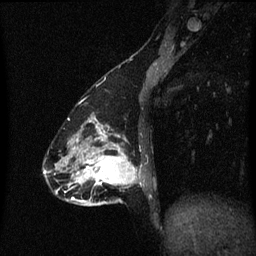
Breast MRI (dynamic contrast-enhanced), one sagittal slice; position 19 of 60 along the scan axis; dynamic contrast-enhanced series, image 2 of 3 at this slice position (ordered by acquisition); 1.5 T; TE 4.2 ms, TR 8.4 ms; 256 × 256 image matrix, field of view 200 × 200 mm. Patient: female, 47 years.
Structures marked on this image (semi-automatic segmentation, software-assisted and operator-edited):
- analysis volume of interest (the breast-tissue region the enhancement analysis was run in; not a lesion): bounding box [x1, y1, x2, y2] px = [81, 138, 145, 207]
- tumour enhancement mask (voxels above the 70 % enhancement threshold inside the analysis volume of interest): [81, 138, 140, 203]